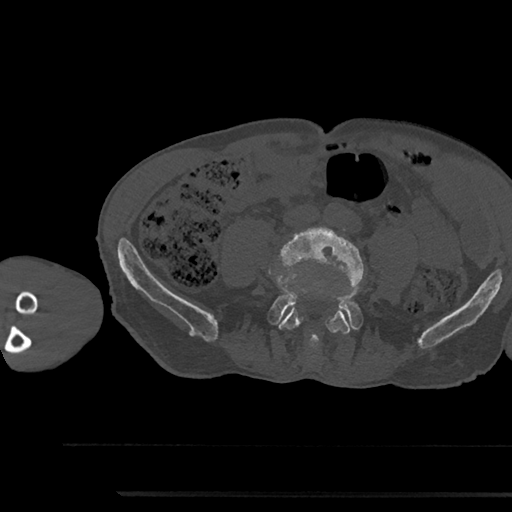
CT including the spine, one axial slice. Position 380 of 797 along the scan axis. Reconstruction kernel Br40s/3. 120 kVp. Bone window (W 1800 / L 400 HU). 0.5 mm slice thickness. 512 × 512 image matrix, field of view 367 × 367 mm. Male patient, age 79 years. Case-level facts recorded for this patient, not image findings: primary cancer: prostate.
Structures marked on this image (semi-automatic segmentation, software-assisted and operator-edited):
- L4 vertebra: bounding box [x1, y1, x2, y2] px = [275, 227, 364, 348]
- L5 vertebra: [270, 292, 362, 346]